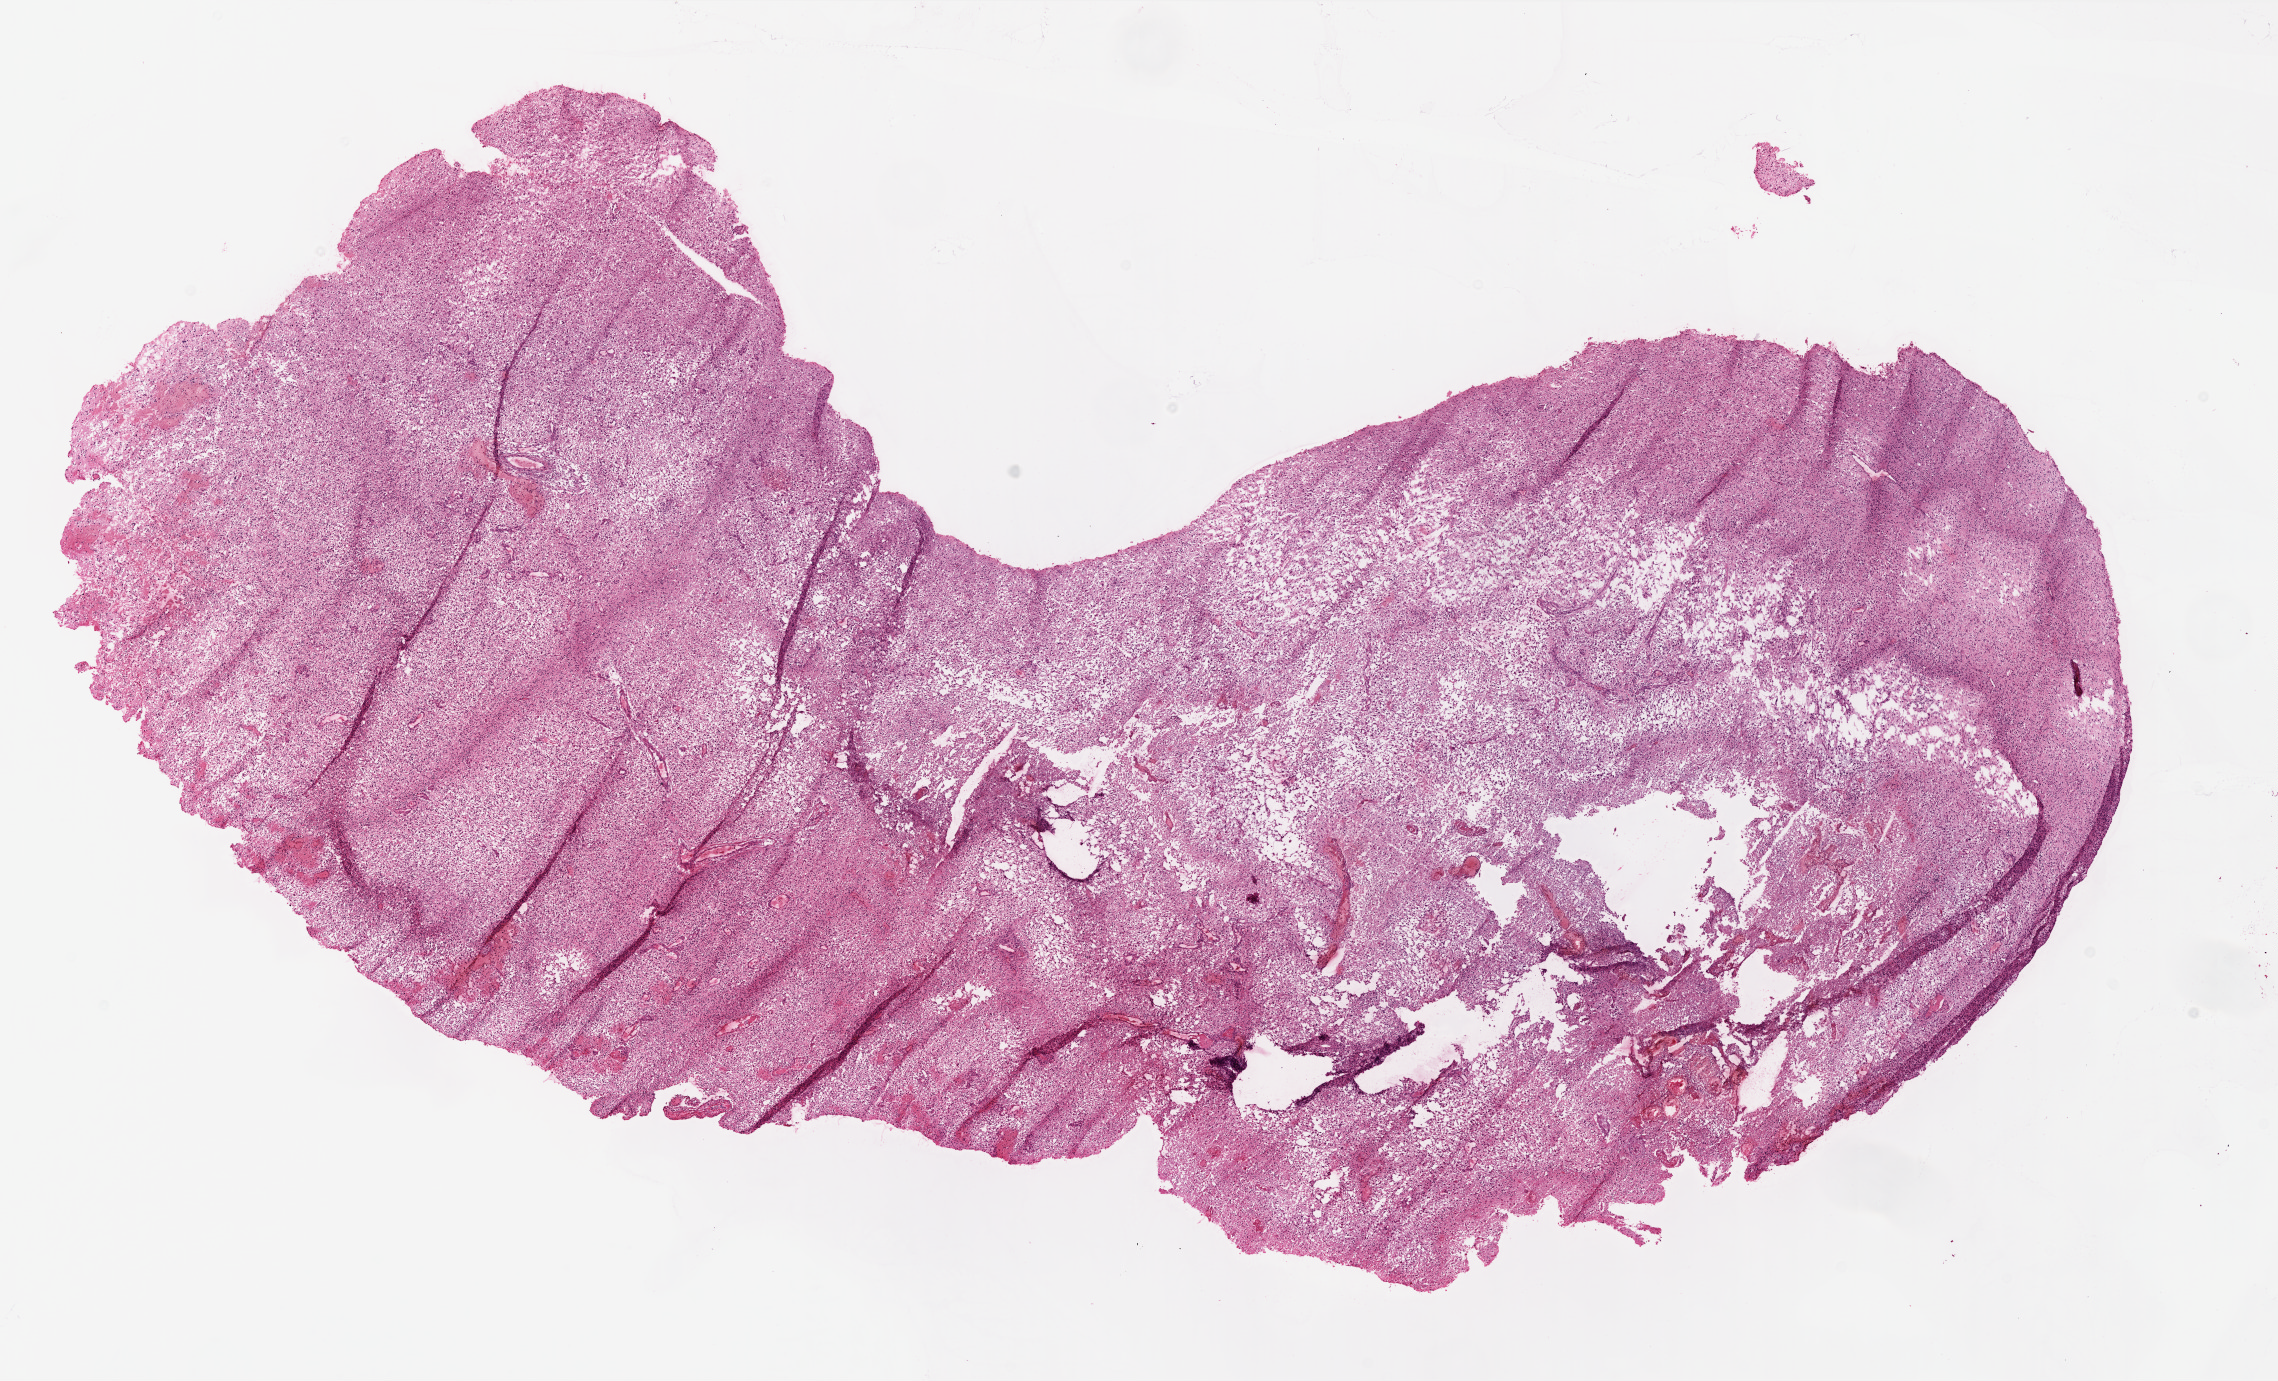
Whole-slide histology image, H&E-stained — whole scanned area (about 18.3 x 11.1 mm) shown as a low-resolution overview, frozen section from the top of the tissue portion, primary tumour sample from the brain. Patient: male, age at initial diagnosis 53 years. Slide review estimates, as recorded: tumour cells 85%, tumour nuclei 100%, normal cells 0%, stromal cells 0%, necrosis 15%.
- diagnosis: Glioblastoma